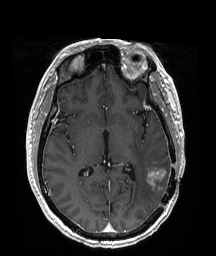
Brain MRI from a brain-tumour surgery series, one axial slice; position 96 of 192 along the scan axis; T1-weighted post-contrast; 1 mm slice thickness; 216 × 256 image matrix. From the clinical record (not read from this slice): histopathology: Glioblastoma; WHO grade: 4; IDH mutation: no; tumour location: Left Temporoparietal.
Annotated regions visible in this slice (outlined manually by an expert reader):
- tumour: bounding box (x1, y1, x2, y2) in pixels: (144, 166, 170, 185)